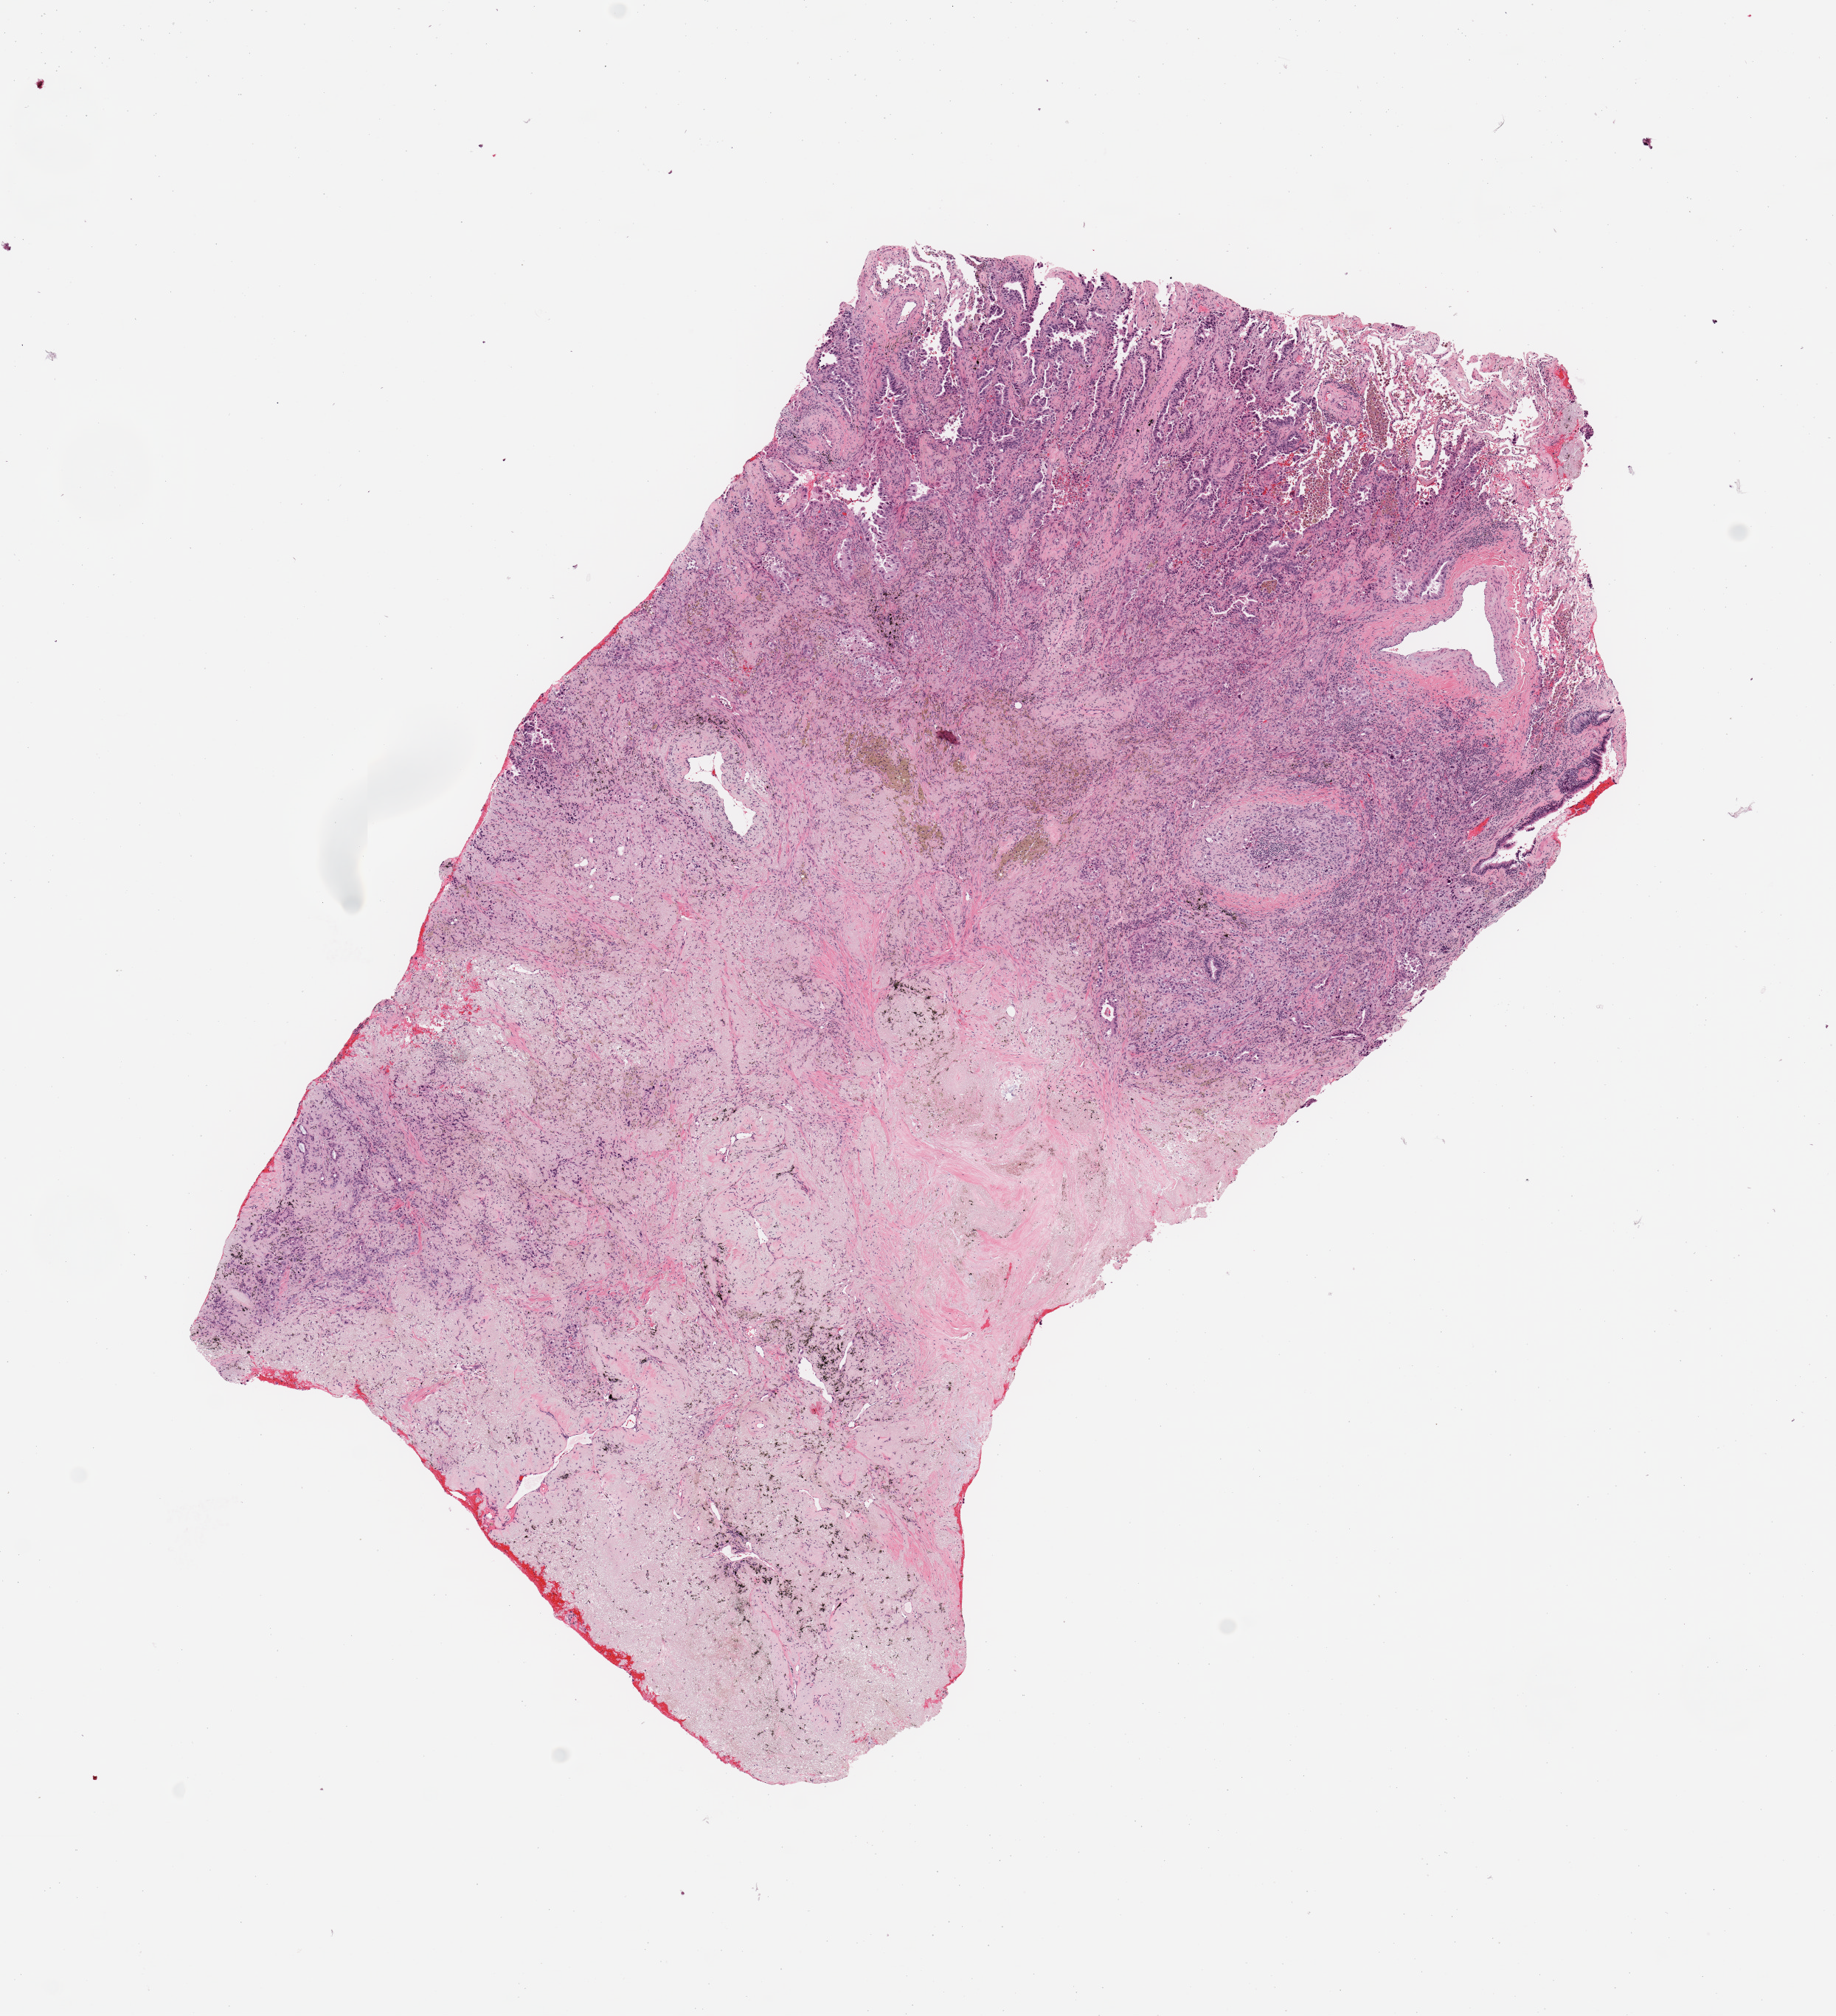
Digitized H&E tissue section (whole slide) — a low-resolution overview of the entire scanned area, about 9.8 x 10.8 mm (acquisition: 20x scan). Tumour tissue sample, sampled site: lung. Patient: male, age 76 years. Histologic grade: G2 (moderately differentiated). Pathologist review of this section (percent, as recorded): tumour nuclei 50%, necrosis 5%.
Histologic diagnosis: Adenocarcinoma, NOS. AJCC pathologic stage: IA. Primary tumour site (as recorded): right upper lobe.